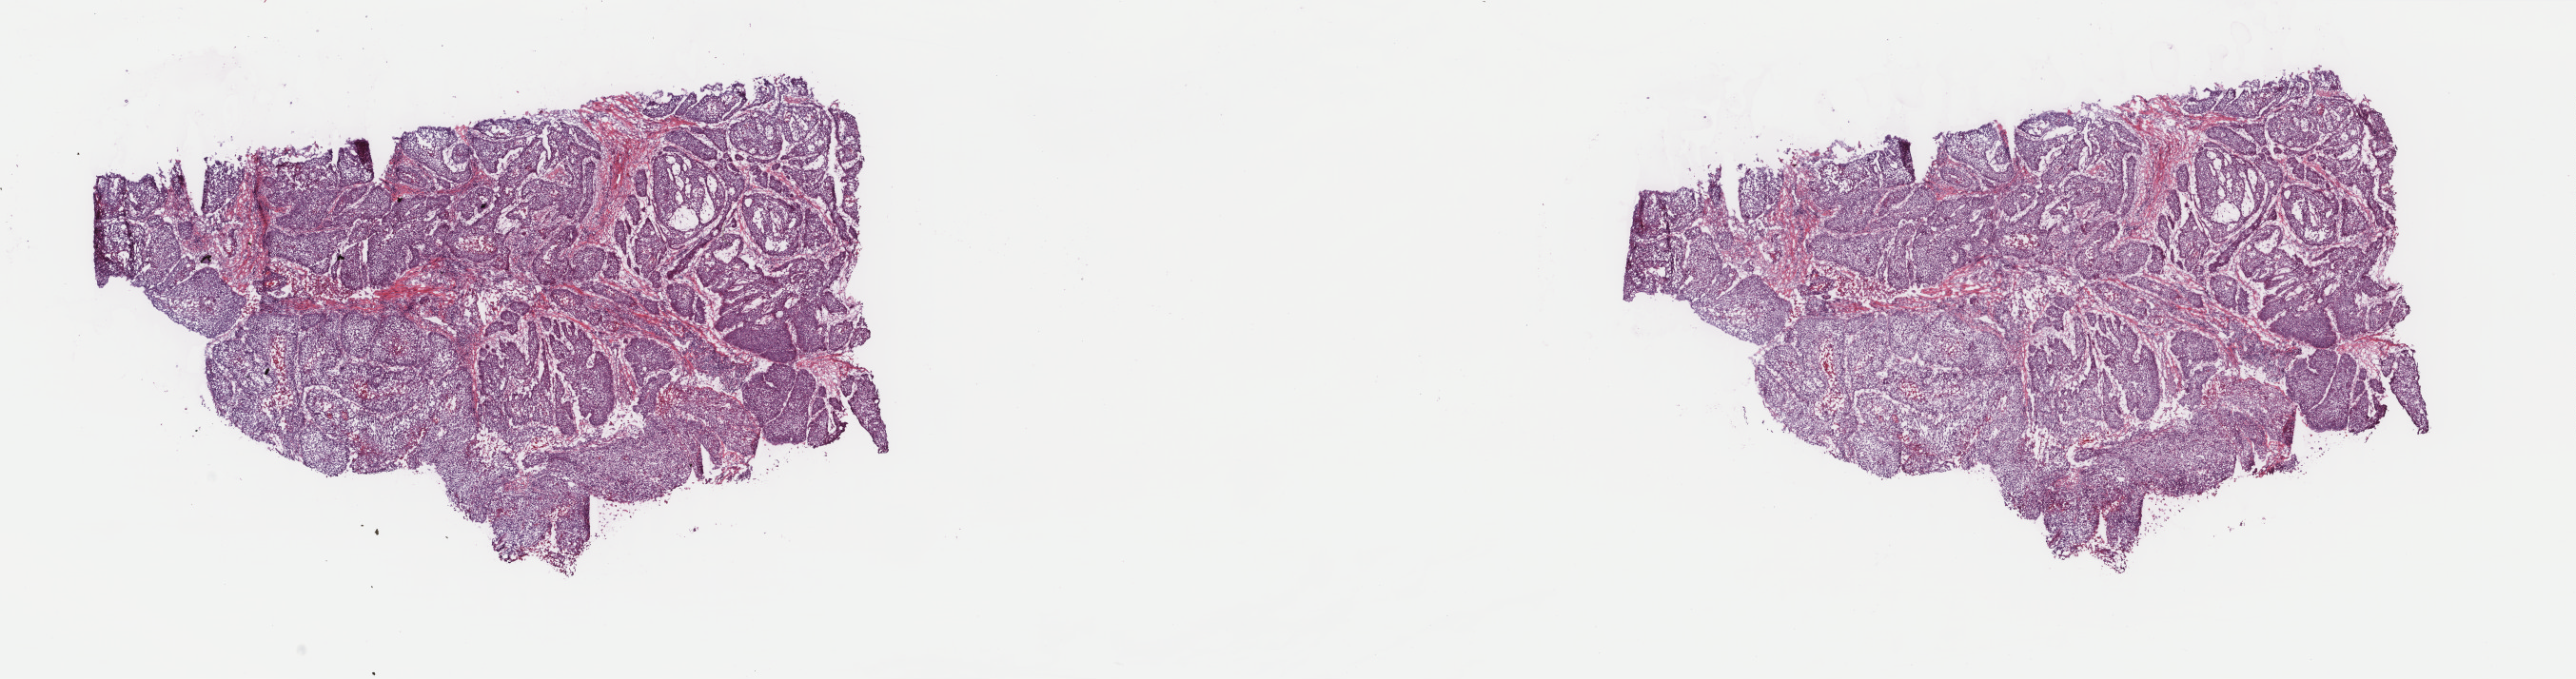
Whole-slide histology image, Hematoxylin and eosin (H&E) stained — whole scanned area (about 21.5 x 5.7 mm) shown as a low-resolution overview, frozen section from the top of the tissue portion, primary tumour sample from the head and neck. Patient: male, age at initial diagnosis 54 years. Histologic grade: G1 (well differentiated). Pathologist review of this section (percent, as recorded): tumour cells 80%, tumour nuclei 90%, normal cells 0%, stromal cells 20%, necrosis 0%. Inflammatory infiltration, as recorded: lymphocyte infiltration 0%, monocyte infiltration 0%, neutrophil infiltration 0%.
AJCC pathologic stage: II (7th edition). Histologic diagnosis: Squamous cell carcinoma, NOS (floor of mouth, NOS). Lymph nodes positive (case pathology): 0 of 13 examined.